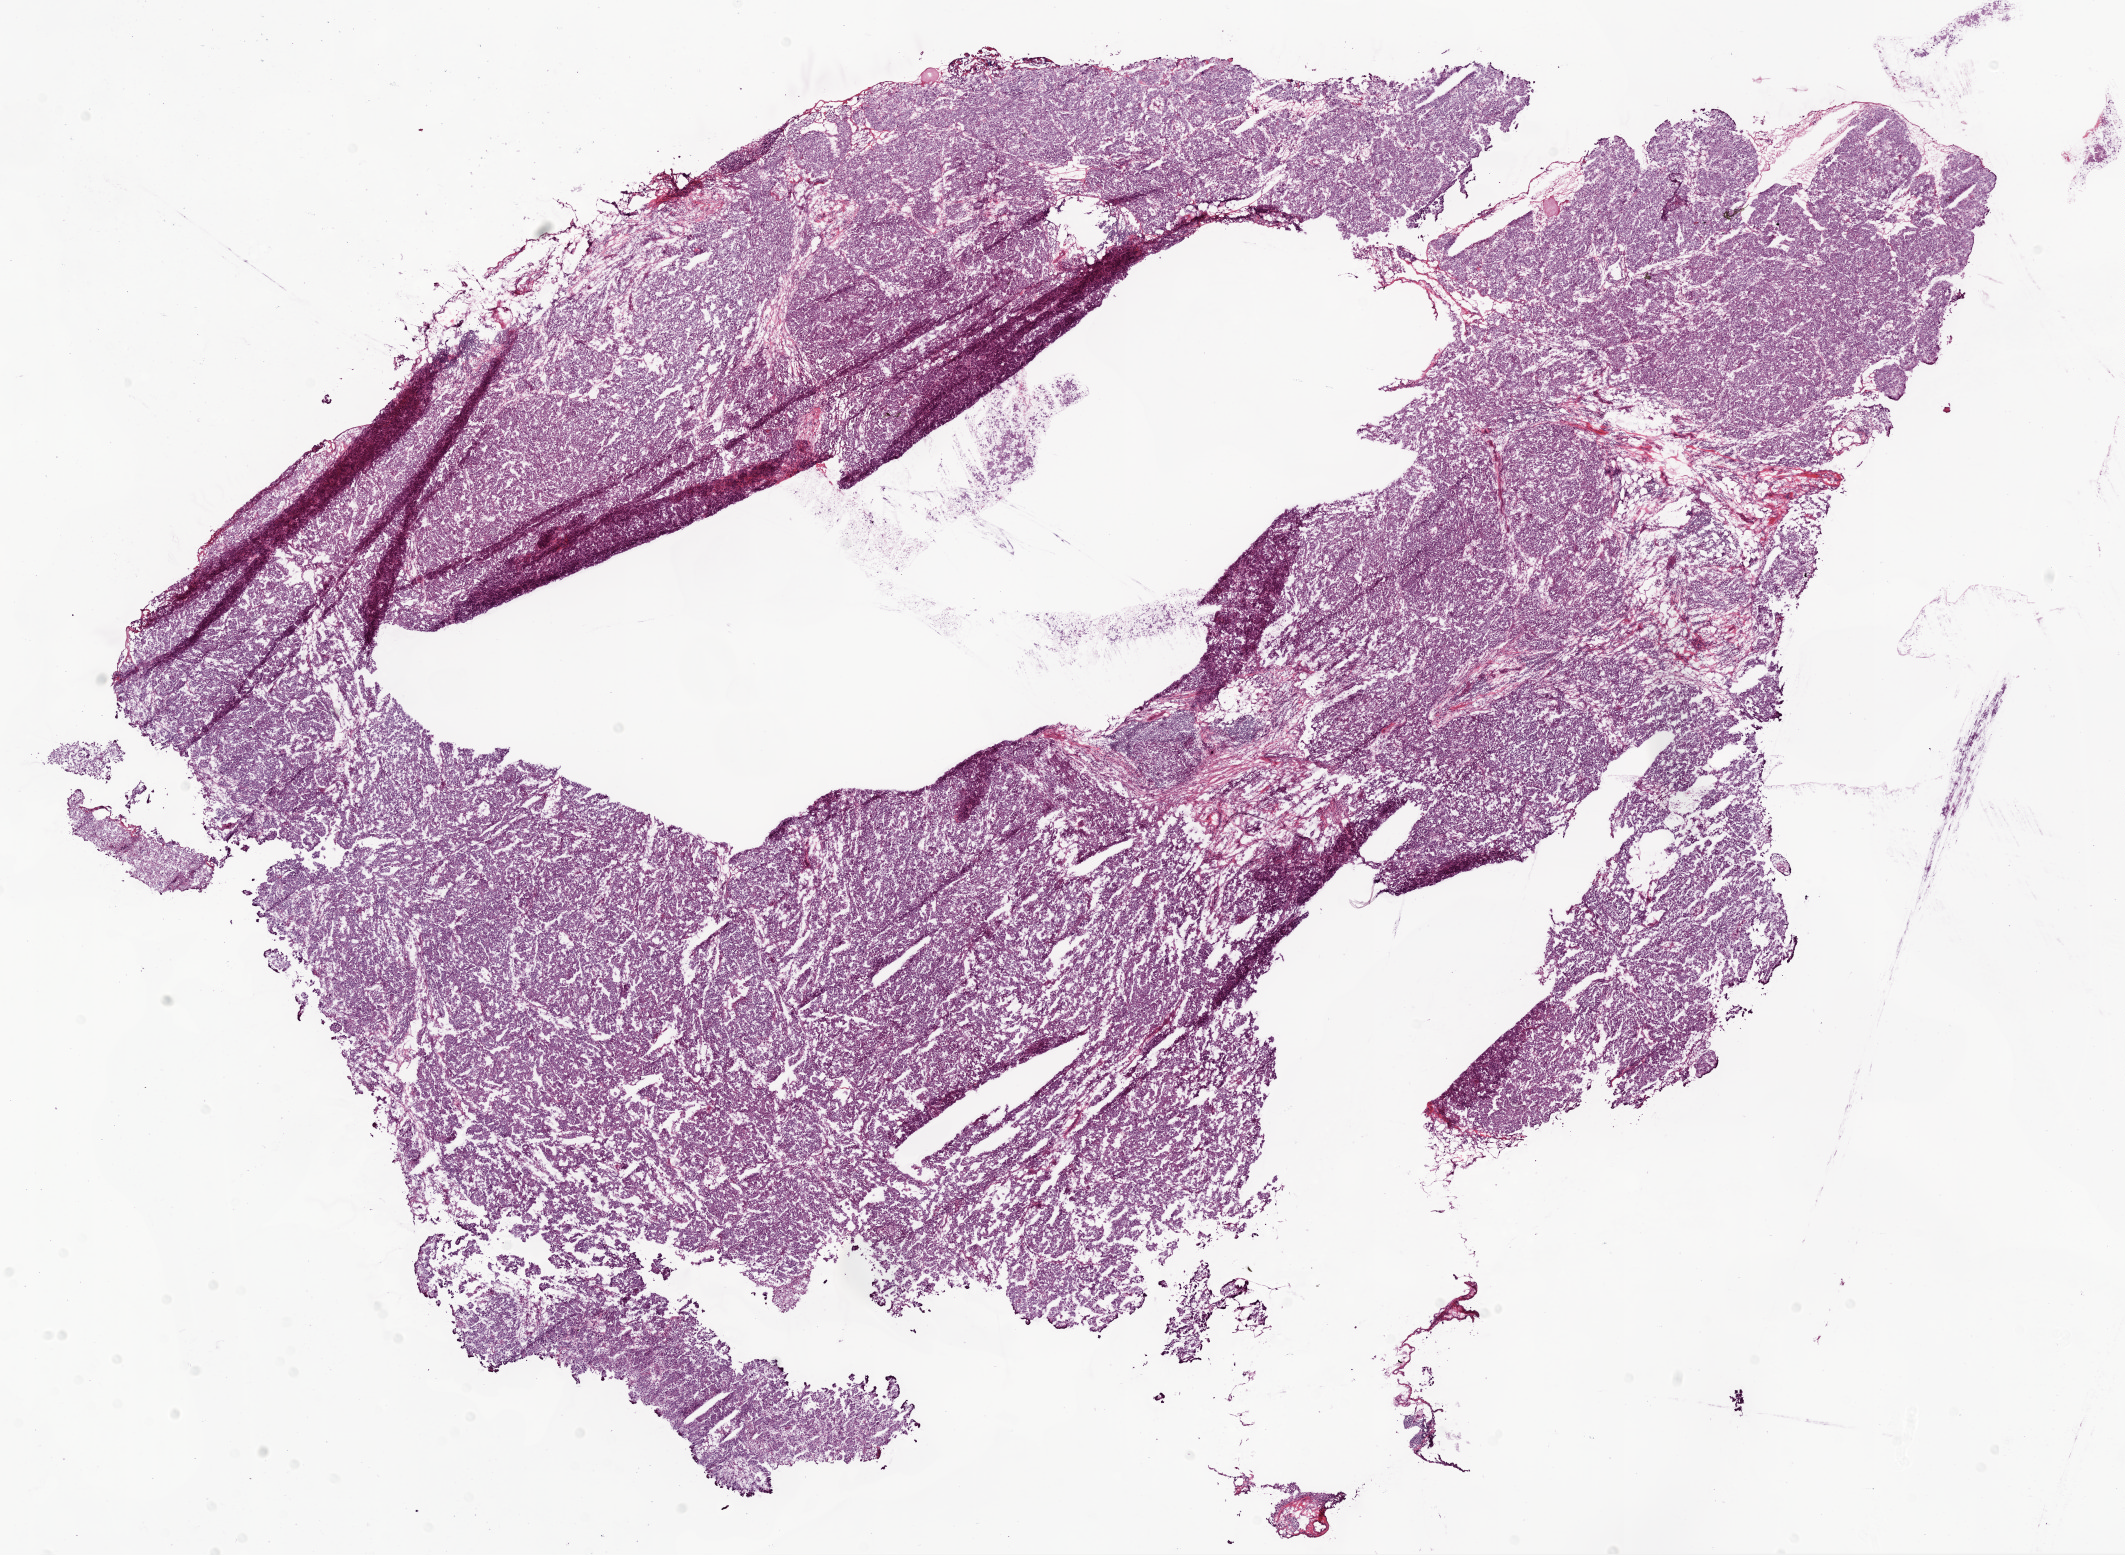
Digitized H&E-stained tissue section (whole slide), shown as a low-resolution overview of the whole scanned area (about 17.1 x 12.5 mm, from a 20x scan). Frozen section from the bottom of the tissue portion. Sample: primary tumour, ovary. Patient: female, age at initial diagnosis 57 years. Histologic grade: G3 (poorly differentiated). Pathologist review of this section (percent, as recorded): tumour cells 98%, tumour nuclei 90%, normal cells 0%, stromal cells 0%, necrosis 2%. Infiltration values recorded for this section: lymphocyte infiltration 5%.
• pathologic diagnosis: Serous cystadenocarcinoma, NOS
• laterality: bilateral
• FIGO stage: IIIC